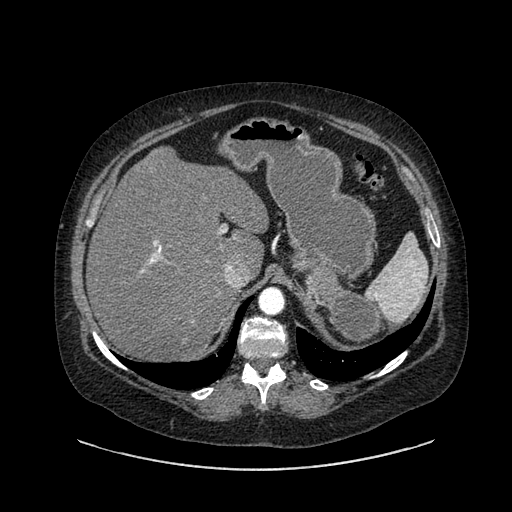
Contrast-enhanced abdominal CT, one axial slice. Position 628 of 769 along the scan axis. Intravenous contrast given. Soft-tissue window (W 400 / L 40 HU). 0.62 mm slice thickness. 512 × 512 image matrix. Patient: female, 61 years. From the clinical record (not read from this slice): diagnosis: adrenocortical carcinoma; tumour side: left adrenal; tumour size at pathology: 13 cm; Ki-67 index: 79 %; stage (as recorded): 2.
Outlined on this slice (semi-automatically segmented with operator editing):
- mass: bounding box (x1, y1, x2, y2) in pixels: (304, 269, 381, 346)